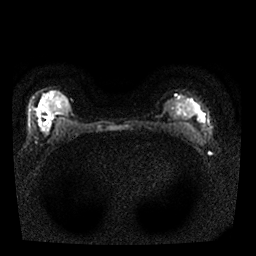
Breast MRI, one axial slice. Position 15 of 25 along the scan axis. Diffusion-weighted series; image 2 of 4 stored at this slice position (different b-values; order by instance number). 1.5 T. 4 mm slice thickness. 256 × 256 image matrix, field of view 310 × 310 mm. Female patient.
Outlined on this slice (expert manual segmentation):
- tumour on diffusion-weighted imaging: bounding box (x1, y1, x2, y2) in pixels: (41, 124, 48, 133)